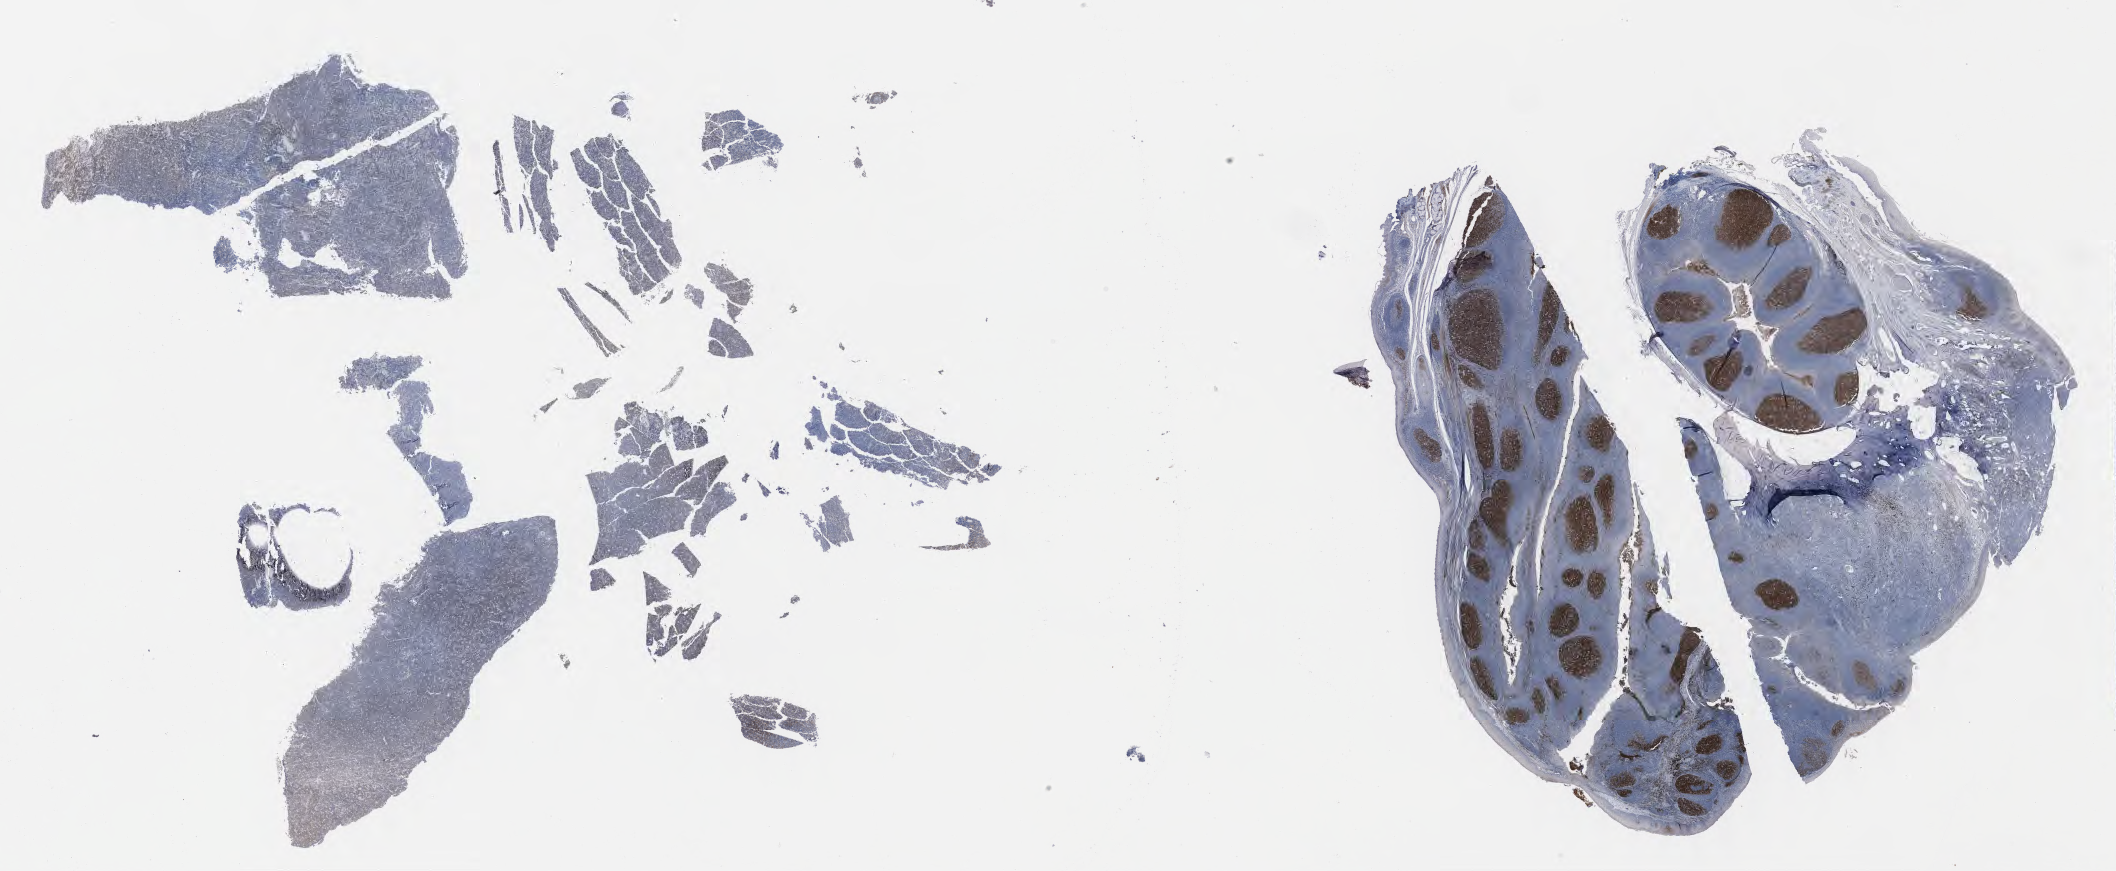
IHC for CD10, whole-slide image, shown as a low-resolution overview of the whole scanned area (about 34.2 x 14.1 mm). Tumor tissue. Male patient; age at initial diagnosis 9 years.
- histologic diagnosis: Burkitt lymphoma, NOS